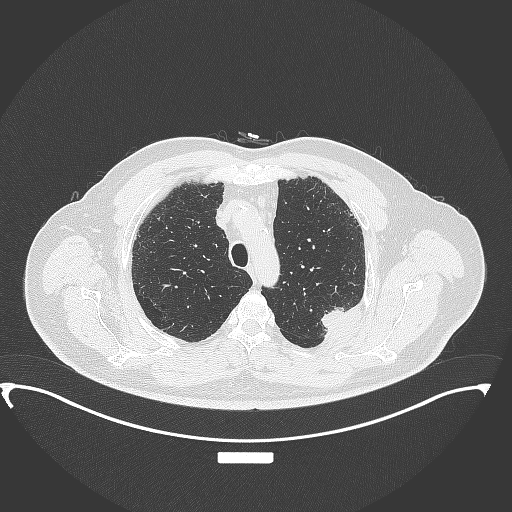
Chest CT, one axial slice. Reconstruction kernel B70f. Lung window (W 1500 / L -600 HU). 1 mm slice thickness. 512 × 512 image matrix. Patient: male, 64 years. Case-level facts recorded for this patient, not image findings: clinical TNM (as recorded): T1c N1 M1.
Annotated regions visible in this slice (rectangle marked by the reading radiologist):
- lung tumour (recorded histology: adenocarcinoma): box from (x=318, y=297) to (x=356, y=341) px